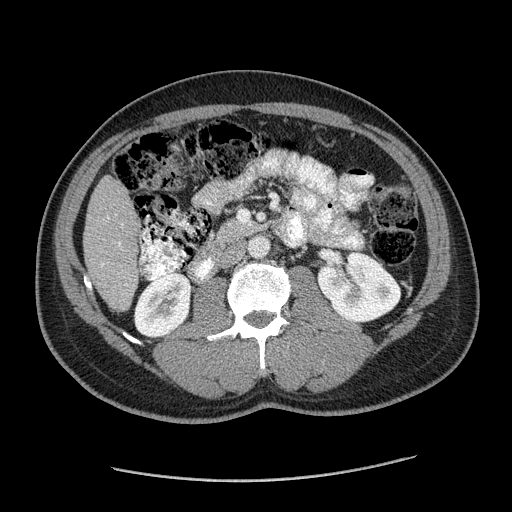
Contrast-enhanced abdominal CT (liver protocol), one axial slice; reconstruction kernel STANDARD; 120 kVp; soft-tissue window (W 400 / L 40 HU); 2.5 mm slice thickness; 512 × 512 image matrix. Case-level facts recorded for this patient, not image findings: diagnosis: hepatocellular carcinoma (patient treated with transarterial chemoembolisation; whether this scan precedes or follows treatment is not stated here); TNM stage (as recorded): Stage-I; Child-Pugh class: A; tumour differentiation: well differentiated; tumour nodularity: uninodular.
Annotated regions visible in this slice (semi-automatically segmented with operator editing):
- liver parenchyma outside the tumour (the mass and vessels are separate outlines, so this box may not span the whole liver): box from (x=84, y=176) to (x=140, y=310) px
- liver vessels: (x=102, y=243)–(x=121, y=266)